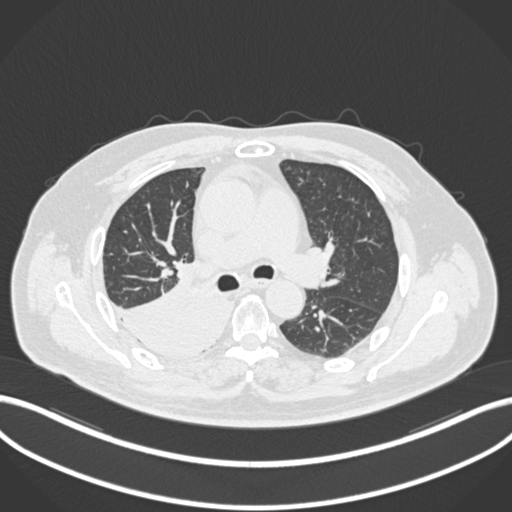
Chest CT, one axial slice; position 122 of 218 along the scan axis; reconstruction kernel B30f; 120 kVp; lung window (W 1500 / L -600 HU); 512 × 512 image matrix. Patient: male, 68 years. Case-level facts recorded for this patient, not image findings: clinical TNM (as recorded): T2a N0 M0.
Annotated regions visible in this slice (rectangle marked by the reading radiologist):
- lung tumour (recorded histology: adenocarcinoma): bounding box <107,278,238,357> (left, top, right, bottom; pixels)